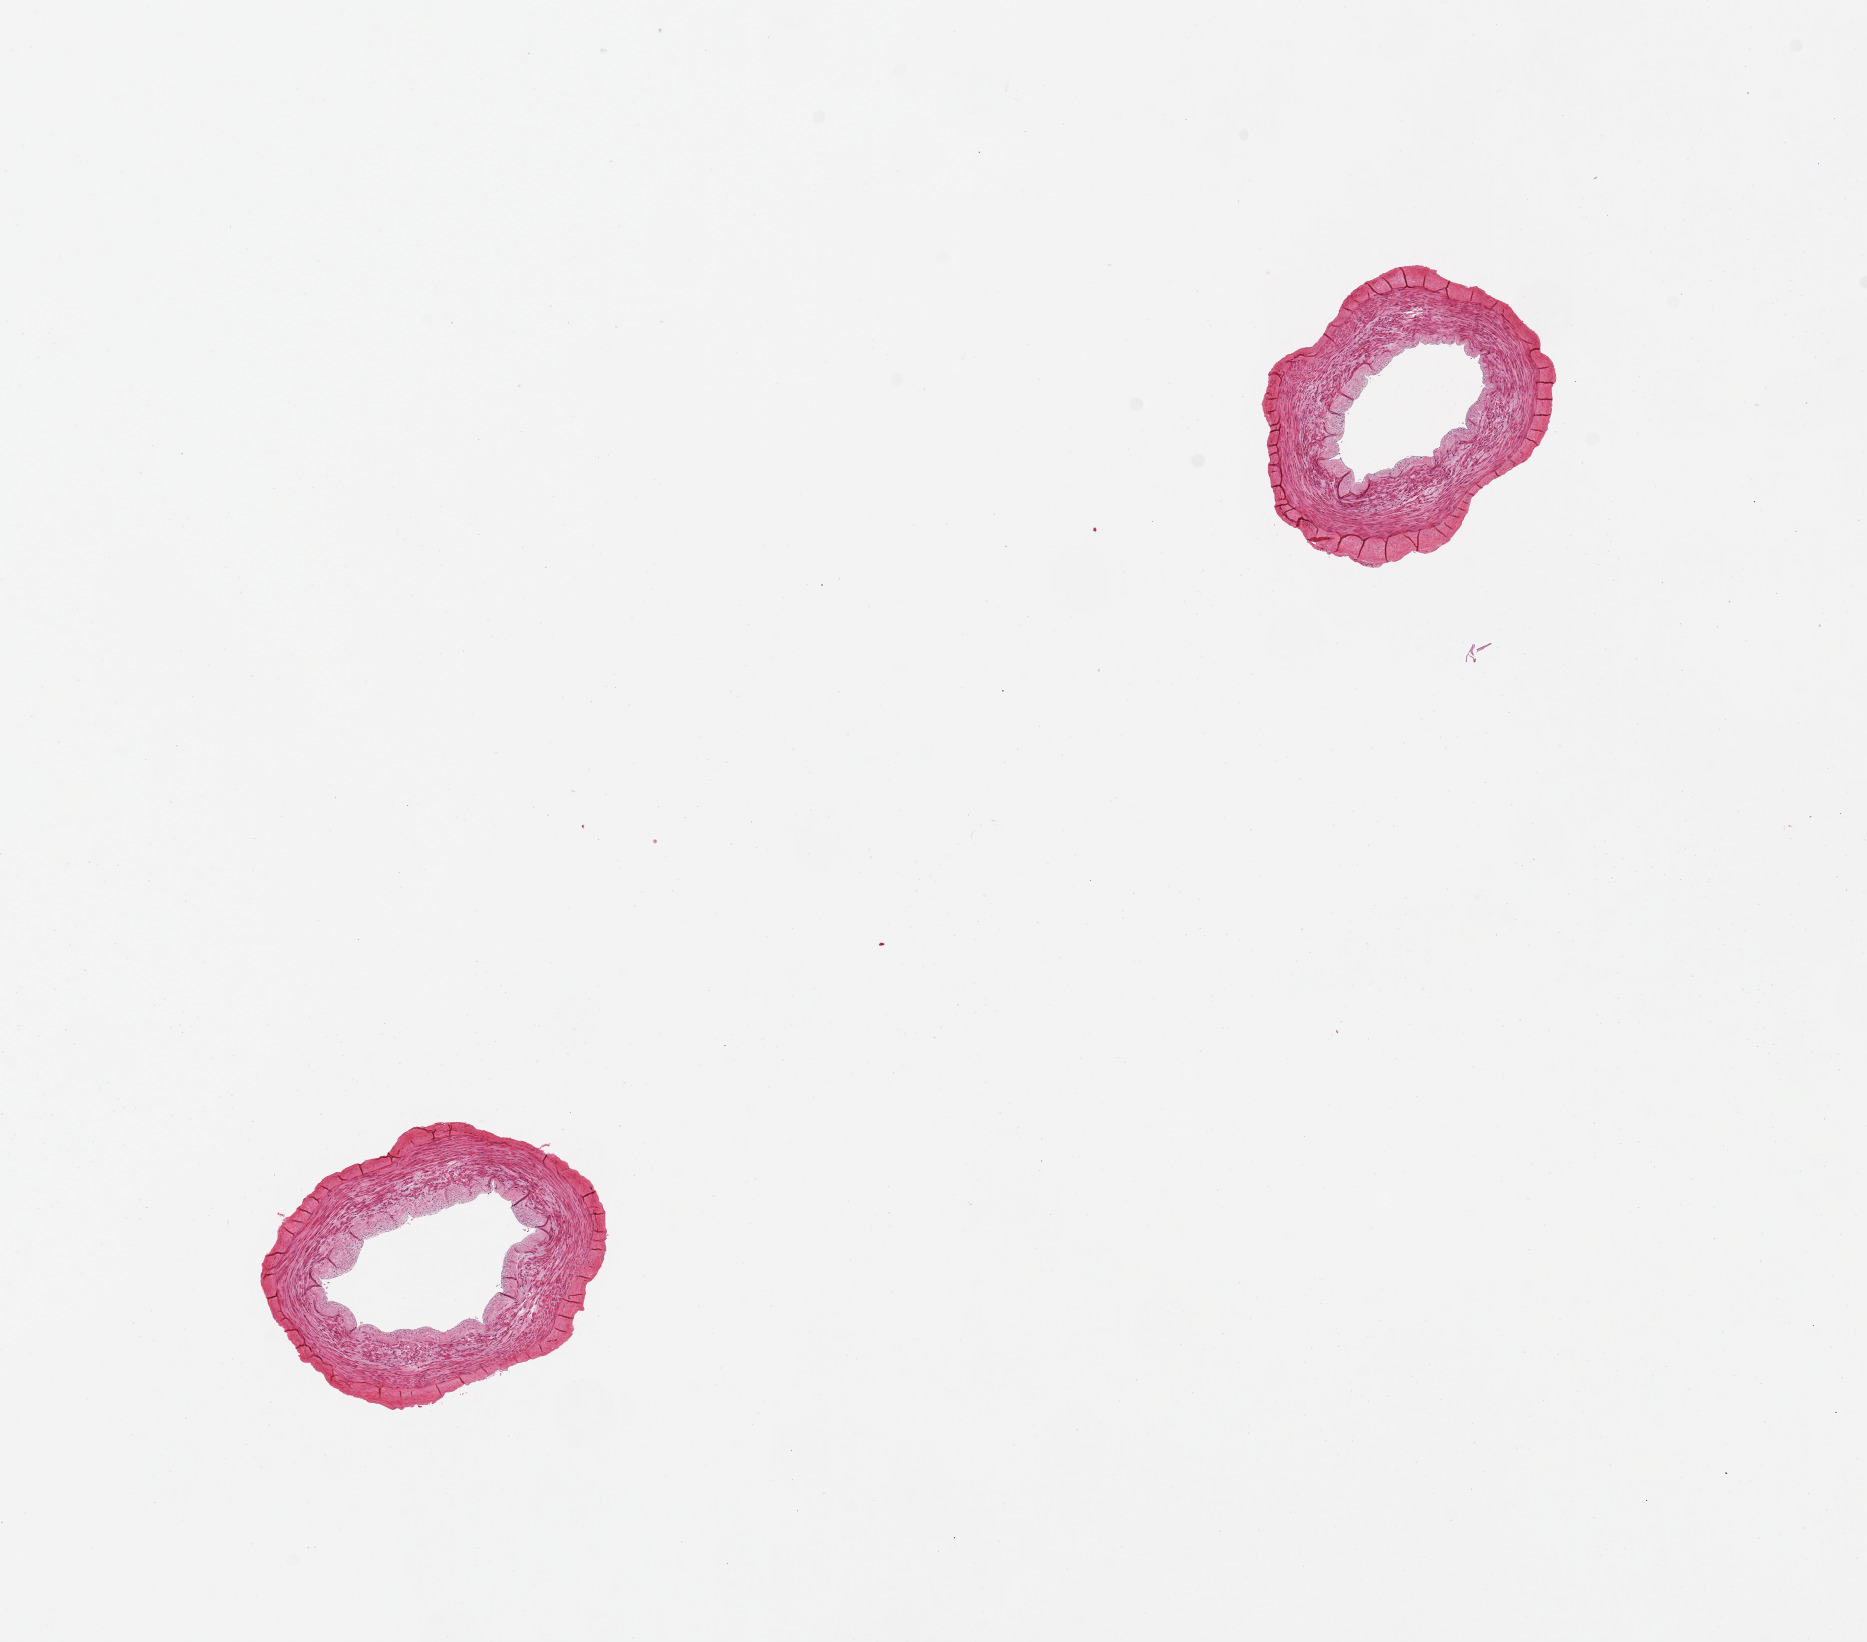
Hematoxylin and eosin (H&E) whole-slide image, whole scanned area (about 14.8 x 13.0 mm, acquisition: 20x scan) shown as a low-resolution overview, PAXgene-fixed paraffin-embedded (PFPE) section, section of tibial artery (target tissue), tissue donor sample. Male donor.
* review note (as recorded): 2 pieces 2 x 2 and 3 x 2 mm. Well trimmed. No lesions